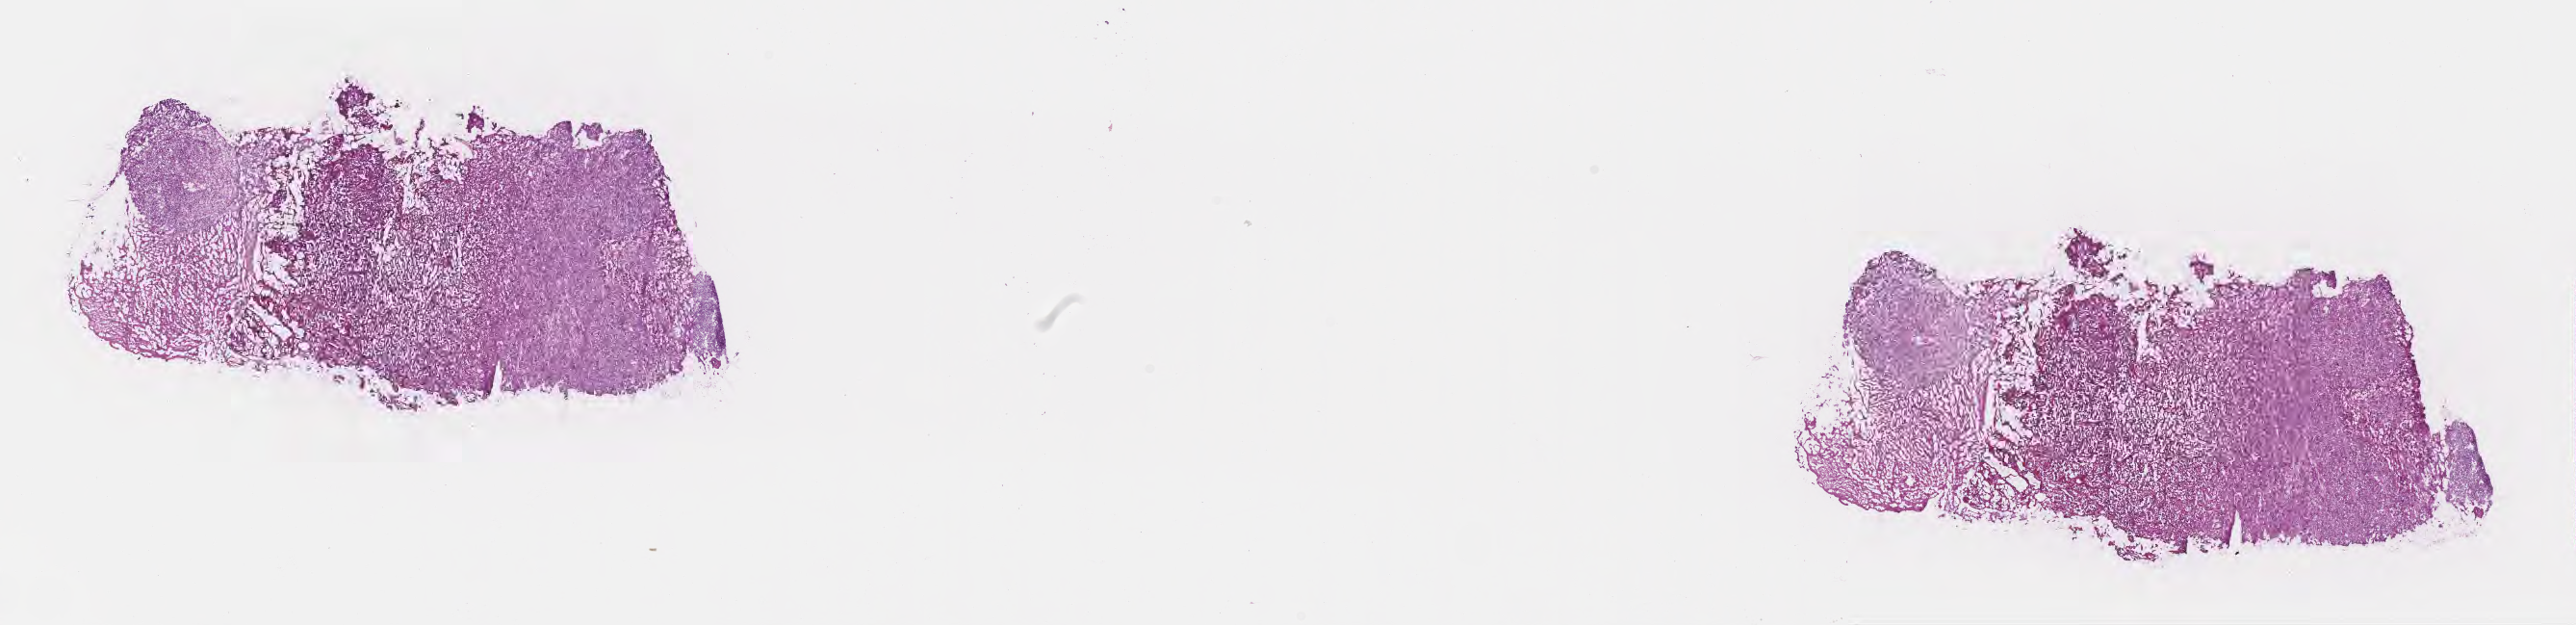
Digitized H&E-stained section, a low-resolution overview of the entire scanned area, about 21.6 x 5.2 mm. Frozen section (snap frozen). Metastatic tumor tissue, resected from brain. Patient: male, age at initial diagnosis 48 years. Pathologist review of this section (percent, as recorded): tumor cells 75%, tumor nuclei 75%, stromal cells 15%, necrosis 10%, normal cells 0%. Infiltration values recorded for this section: lymphocyte infiltration 3%, monocyte infiltration 3%, neutrophil infiltration 4%.
- section: bottom of the tissue portion
- patient diagnosis (primary): Carcinoma, NOS